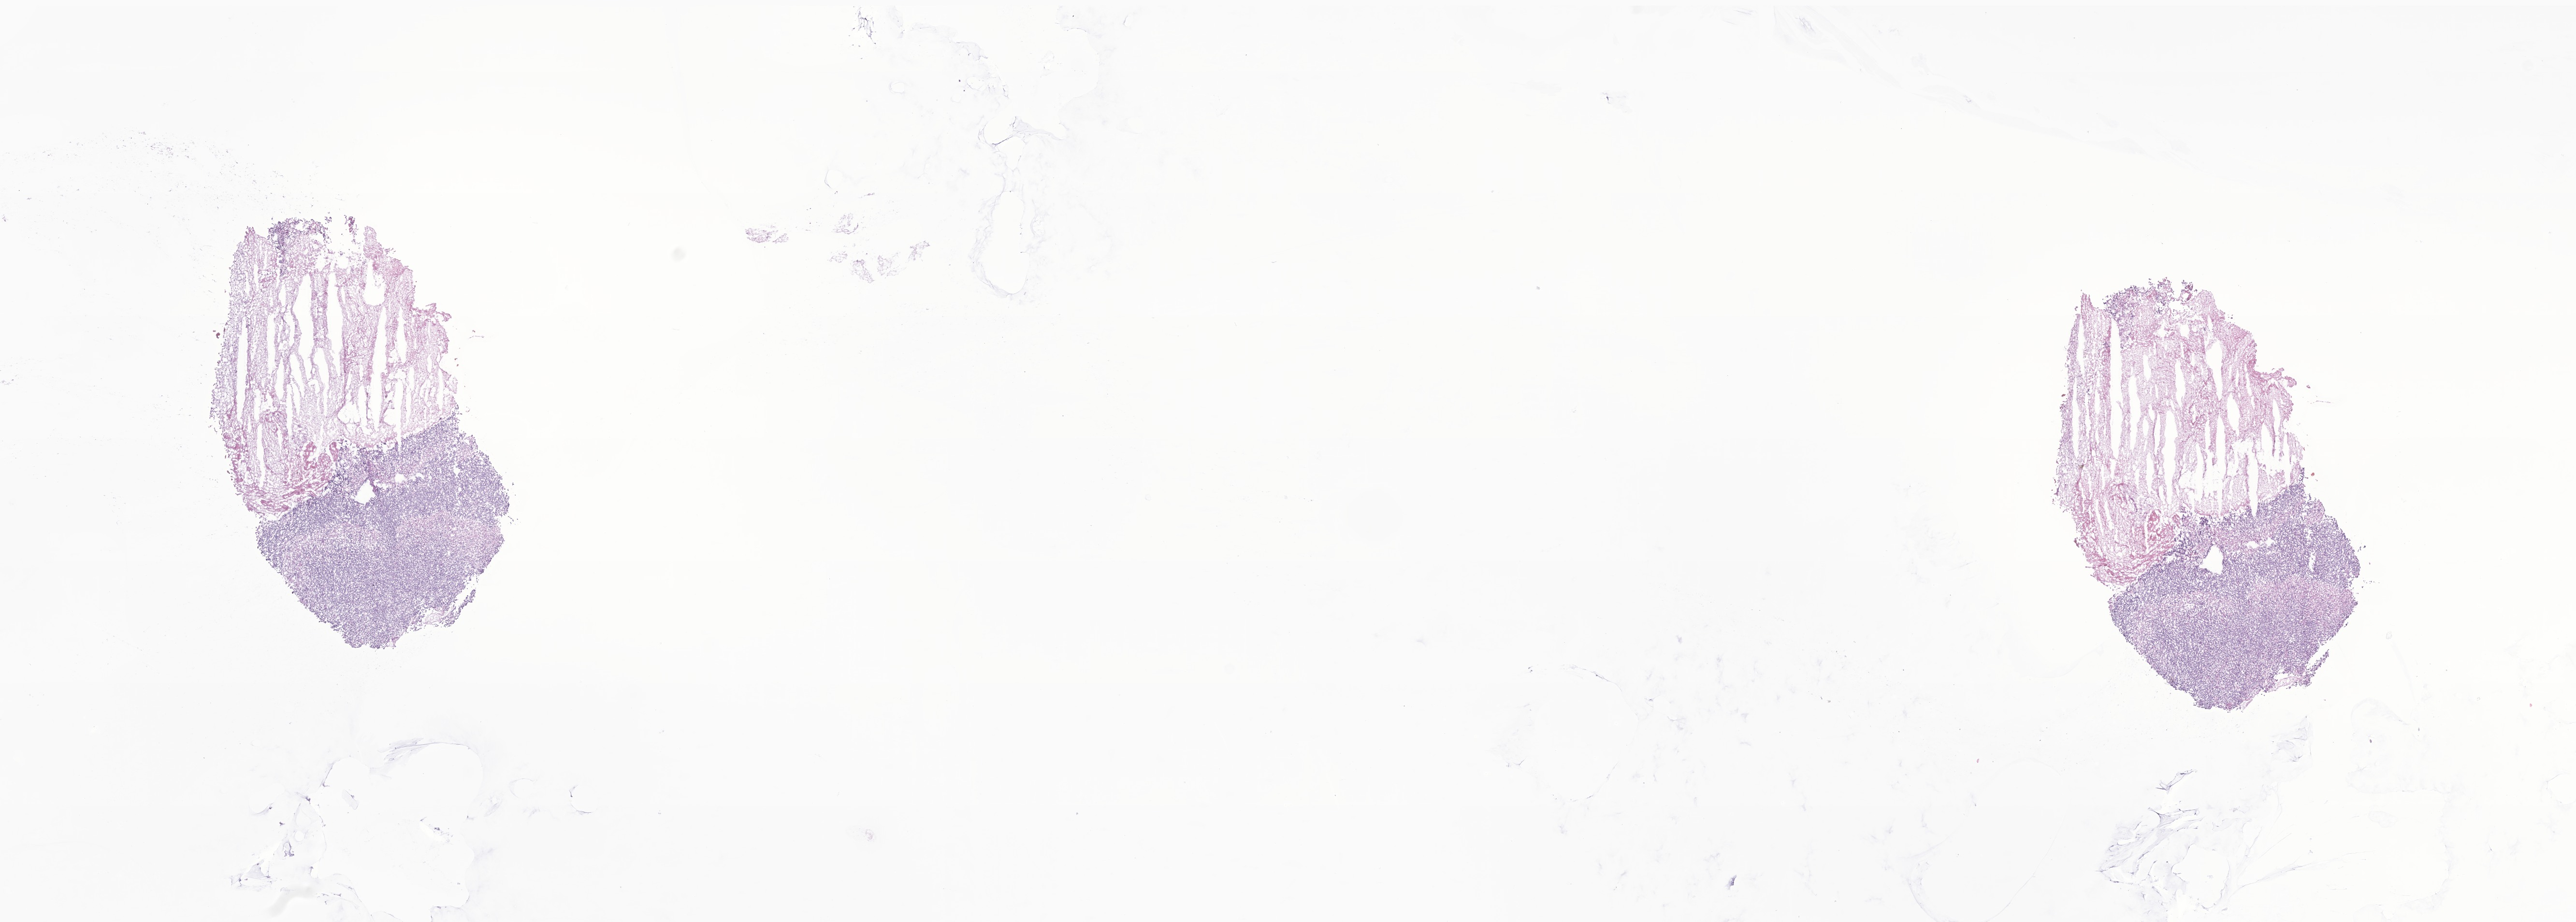
Whole-slide image, H&E stain of tumor tissue from the brain — low-resolution overview of the scanned area, about 22.5 x 8.0 mm, cryosection (OCT / tissue freezing medium). Patient: female, age 102 months (8 years 6 months).
Recorded diagnosis: Medulloblastoma, NOS.